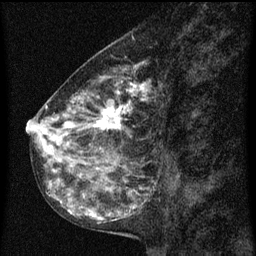
Breast MRI (dynamic contrast-enhanced), one sagittal slice; dynamic contrast-enhanced series, image 2 of 3 at this slice position (ordered by acquisition); 1.5 T; TE 4.2 ms, TR 8 ms; 256 × 256 image matrix, field of view 180 × 180 mm. Patient: female, 55 years.
Structures marked on this image (semi-automatic segmentation, software-assisted and operator-edited):
- analysis volume of interest (the breast-tissue region the enhancement analysis was run in; not a lesion): bounding box <34,68,159,151> (left, top, right, bottom; pixels)
- tumour enhancement mask (voxels above the 70 % enhancement threshold inside the analysis volume of interest): <38,76,151,145>